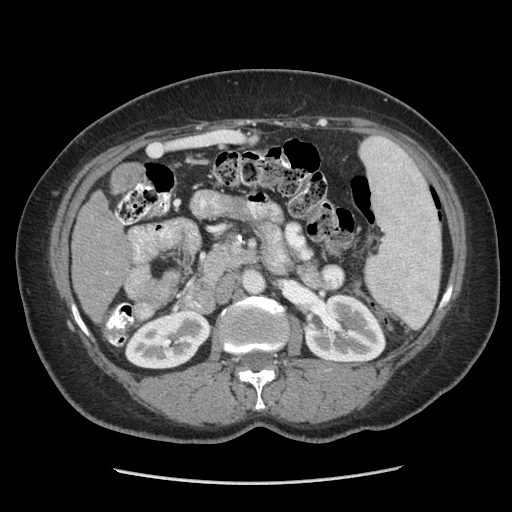
Contrast-enhanced abdominal CT (liver protocol), one axial slice; position 127 of 185 along the scan axis; reconstruction kernel STANDARD; 140 kVp; soft-tissue window (W 400 / L 40 HU); 2.5 mm slice thickness; 512 × 512 image matrix, field of view 360 × 360 mm. From the clinical record (not read from this slice): diagnosis: hepatocellular carcinoma (patient treated with transarterial chemoembolisation; whether this scan precedes or follows treatment is not stated here); TNM stage (as recorded): Stage-I; Child-Pugh class: A; tumour differentiation: poorly differentiated; tumour nodularity: uninodular.
Annotated regions visible in this slice (semi-automatically segmented with operator editing):
- liver parenchyma outside the tumour (the mass and vessels are separate outlines, so this box may not span the whole liver): bounding box (x1, y1, x2, y2) in pixels: (72, 192, 130, 316)
- mass: (111, 164, 140, 193)